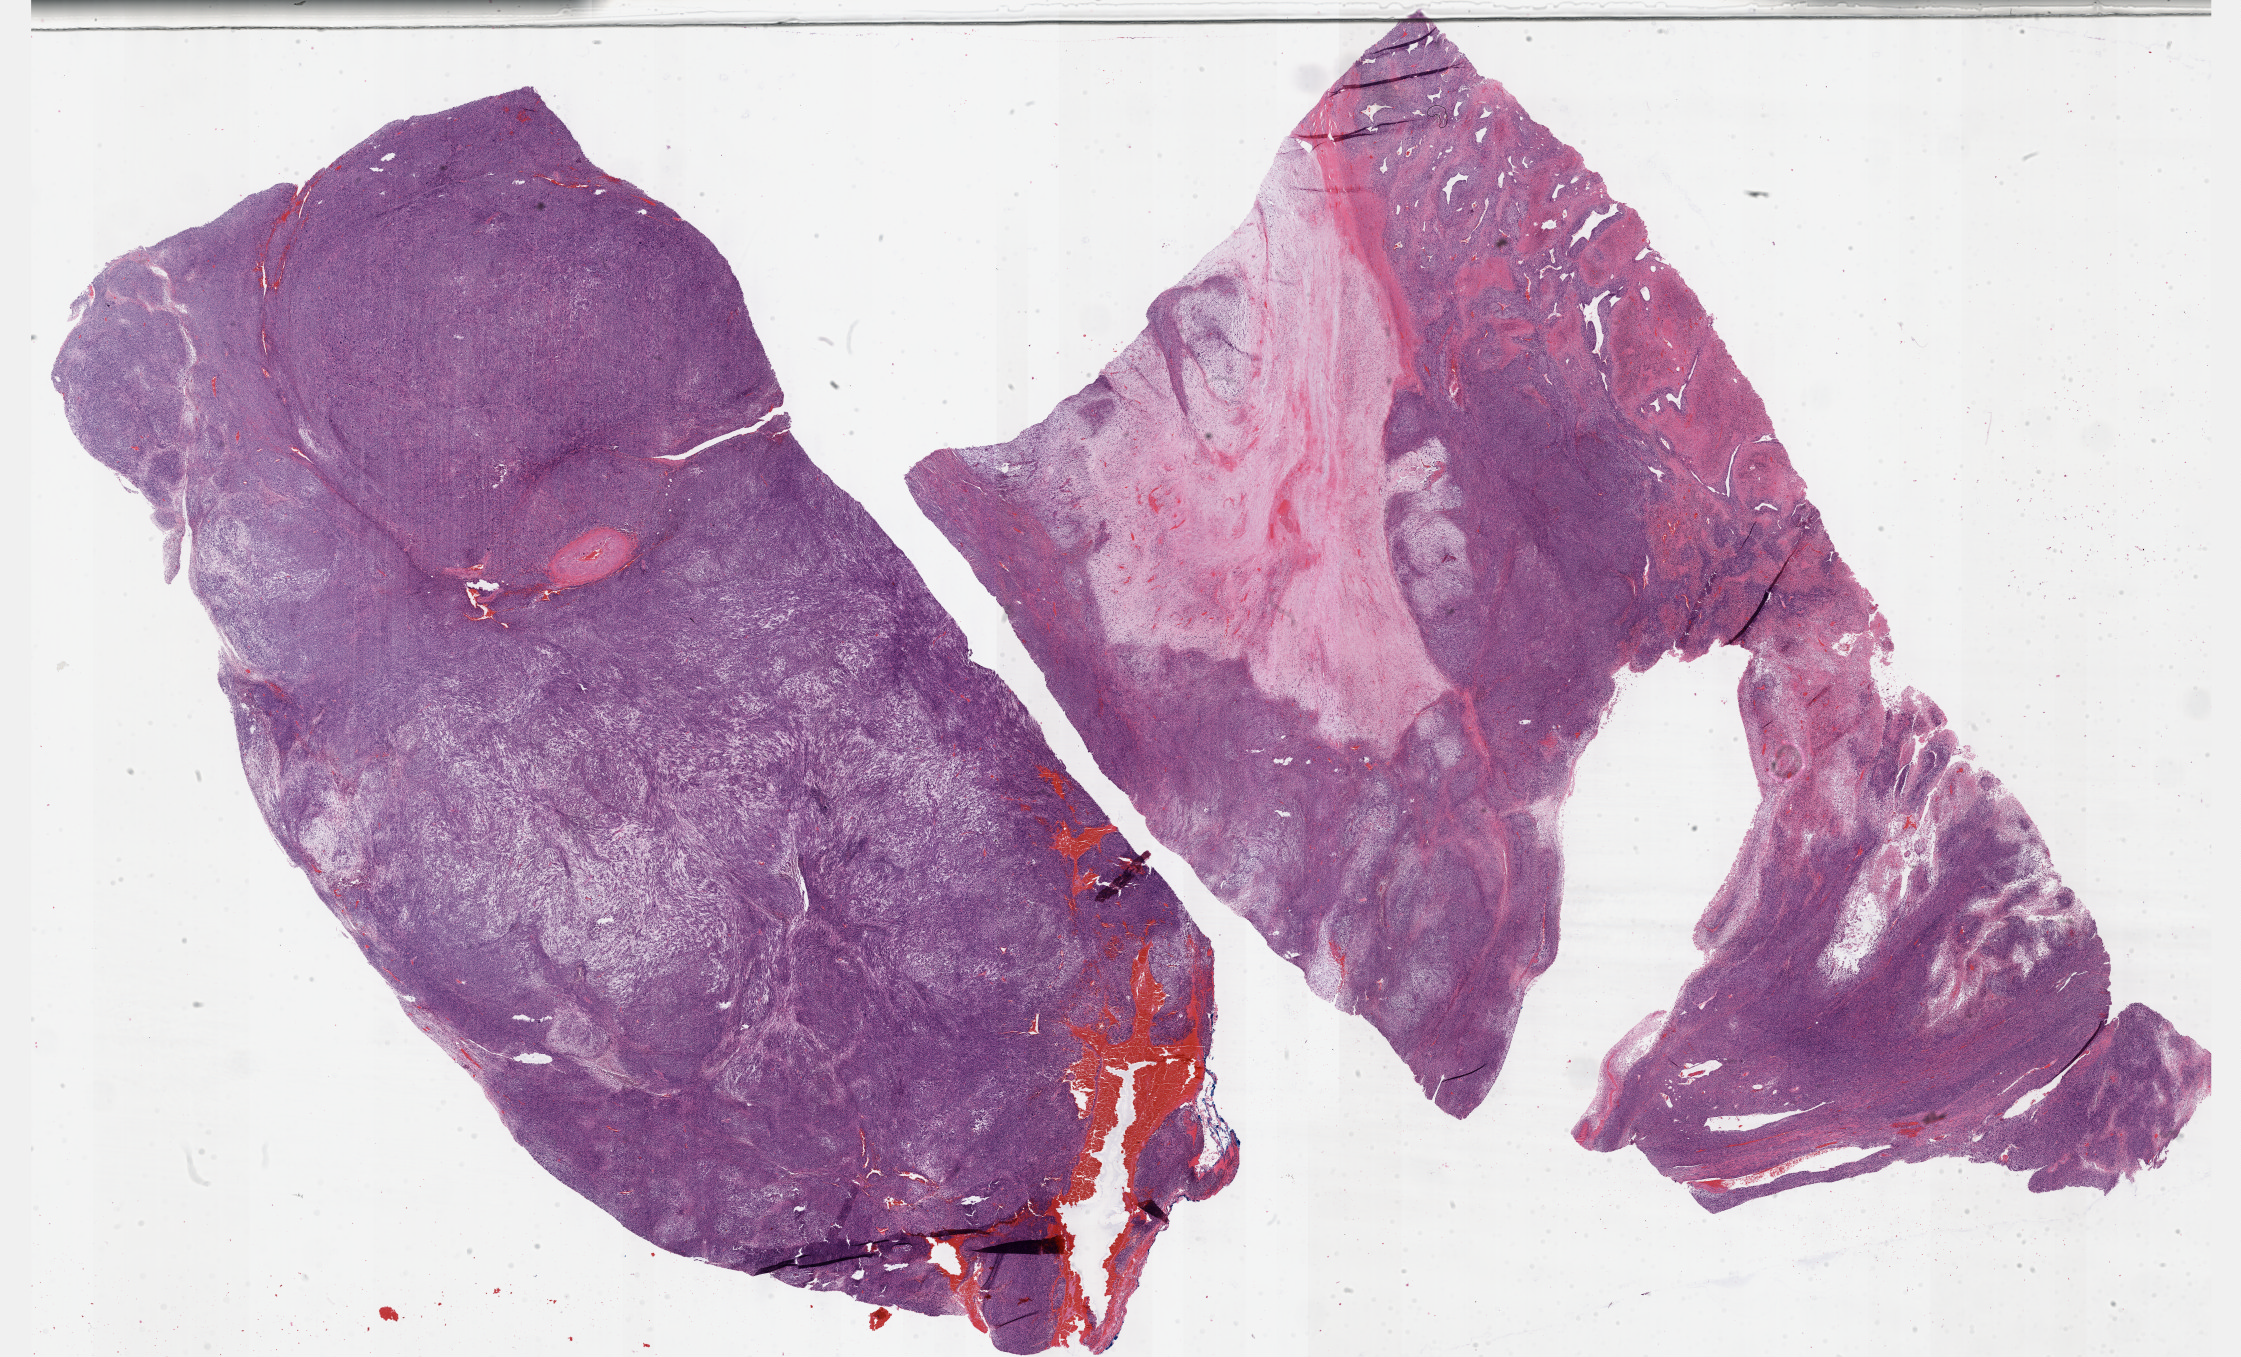
Digitized H&E tissue section (whole slide), a low-resolution overview of the entire scanned area, about 36.2 x 21.9 mm (from a 40x scan). Formalin-fixed paraffin-embedded (FFPE) diagnostic section. Connective, subcutaneous and other soft tissues, primary tumour sample. Female patient; age at initial diagnosis 70 years.
Diagnosis: Undifferentiated sarcoma (connective, subcutaneous and other soft tissues of lower limb and hip).